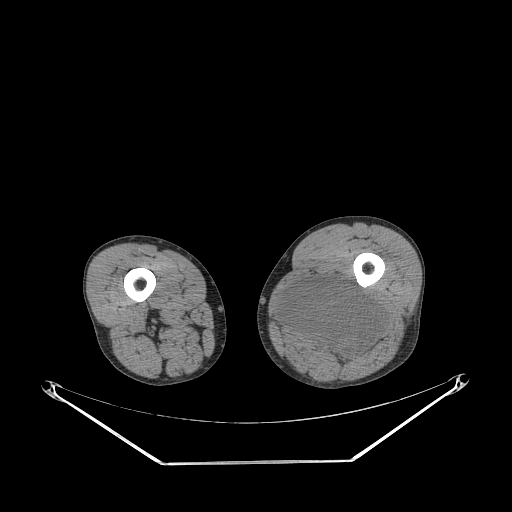
CT of an extremity soft-tissue mass (from a PET/CT study), one axial slice. Slice 225 of 267 in the series (ordered by position). Reconstruction kernel STANDARD. 140 kVp. Soft-tissue window (W 400 / L 40 HU). 3.75 mm slice thickness. 512 × 512 image matrix, field of view 500 × 500 mm. Male patient. Case-level facts recorded for this patient, not image findings: histological type: undifferentiated pleomorphic liposarcoma; grade: high; site of the primary tumour: left thigh.
Structures marked on this image (expert contour drawn on MRI and transferred to this co-registered scan by the dataset authors):
- gross tumour volume including surrounding oedema: bounding box [x1, y1, x2, y2] px = [279, 278, 385, 362]
- gross tumour volume (mass): [281, 278, 385, 362]